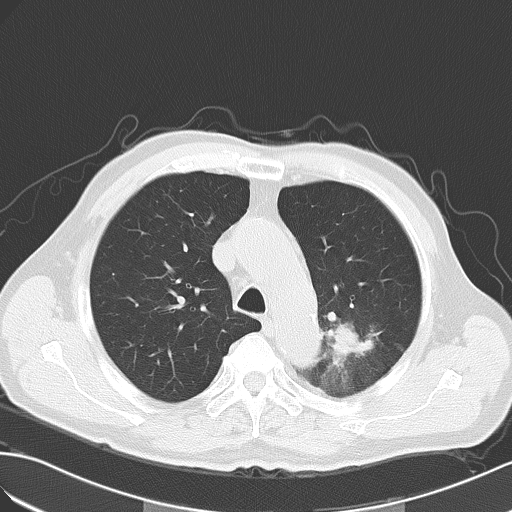
Chest CT, one axial slice. Position 42 of 55 along the scan axis. 120 kVp. Lung window (W 1500 / L -600 HU). 5 mm slice thickness. 512 × 512 image matrix. Male patient, age 63 years. Case-level facts recorded for this patient, not image findings: clinical TNM (as recorded): T3 N3 M1a.
Structures marked on this image (rectangle marked by the reading radiologist):
- lung tumour (recorded histology: large cell carcinoma): bounding box [x1, y1, x2, y2] px = [322, 315, 375, 373]